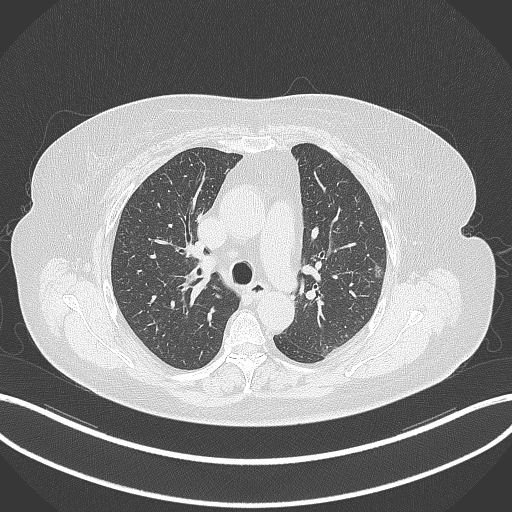
Chest CT, one axial slice; slice 213 of 309 in the series (ordered by position); reconstruction kernel B70f; lung window (W 1500 / L -600 HU); 1 mm slice thickness; 512 × 512 image matrix, field of view 400 × 400 mm. Patient: female, 70 years. From the clinical record (not read from this slice): clinical TNM (as recorded): T1c N0 M0.
Annotated regions visible in this slice (bounding box drawn by a radiologist):
- lung tumour (recorded histology: adenocarcinoma): bounding box <373,257,383,284> (left, top, right, bottom; pixels)